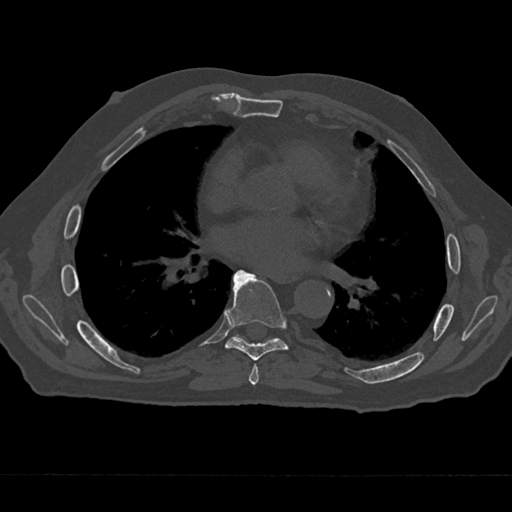
CT including the spine, one axial slice; position 365 of 797 along the scan axis; reconstruction kernel Br40s/3; 120 kVp; bone window (W 1800 / L 400 HU); 0.5 mm slice thickness; 512 × 512 image matrix. Male patient, age 75 years. Case-level facts recorded for this patient, not image findings: primary cancer: renal.
Annotated regions visible in this slice (semi-automatically segmented with operator editing):
- T6 vertebra: box from (x=249, y=364) to (x=259, y=385) px
- T7 vertebra: (x=226, y=270)–(x=288, y=361)